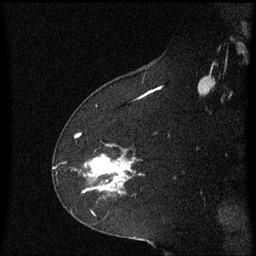
Breast MRI (dynamic contrast-enhanced), one sagittal slice; position 39 of 60 along the scan axis; dynamic contrast-enhanced series, image 2 of 3 at this slice position (ordered by acquisition); 1.5 T; TE 4.2 ms, TR 8.4 ms; 256 × 256 image matrix, field of view 200 × 200 mm. Female patient, age 60 years. From the clinical record (not read from this slice): setting: breast cancer imaged before/during neoadjuvant chemotherapy; receptor status: triple-negative.
Outlined on this slice (semi-automatic segmentation, software-assisted and operator-edited):
- analysis volume of interest (the breast-tissue region the enhancement analysis was run in; not a lesion): bounding box (x1, y1, x2, y2) in pixels: (76, 144, 143, 199)
- tumour enhancement mask (voxels above the 70 % enhancement threshold inside the analysis volume of interest): (85, 156, 132, 191)